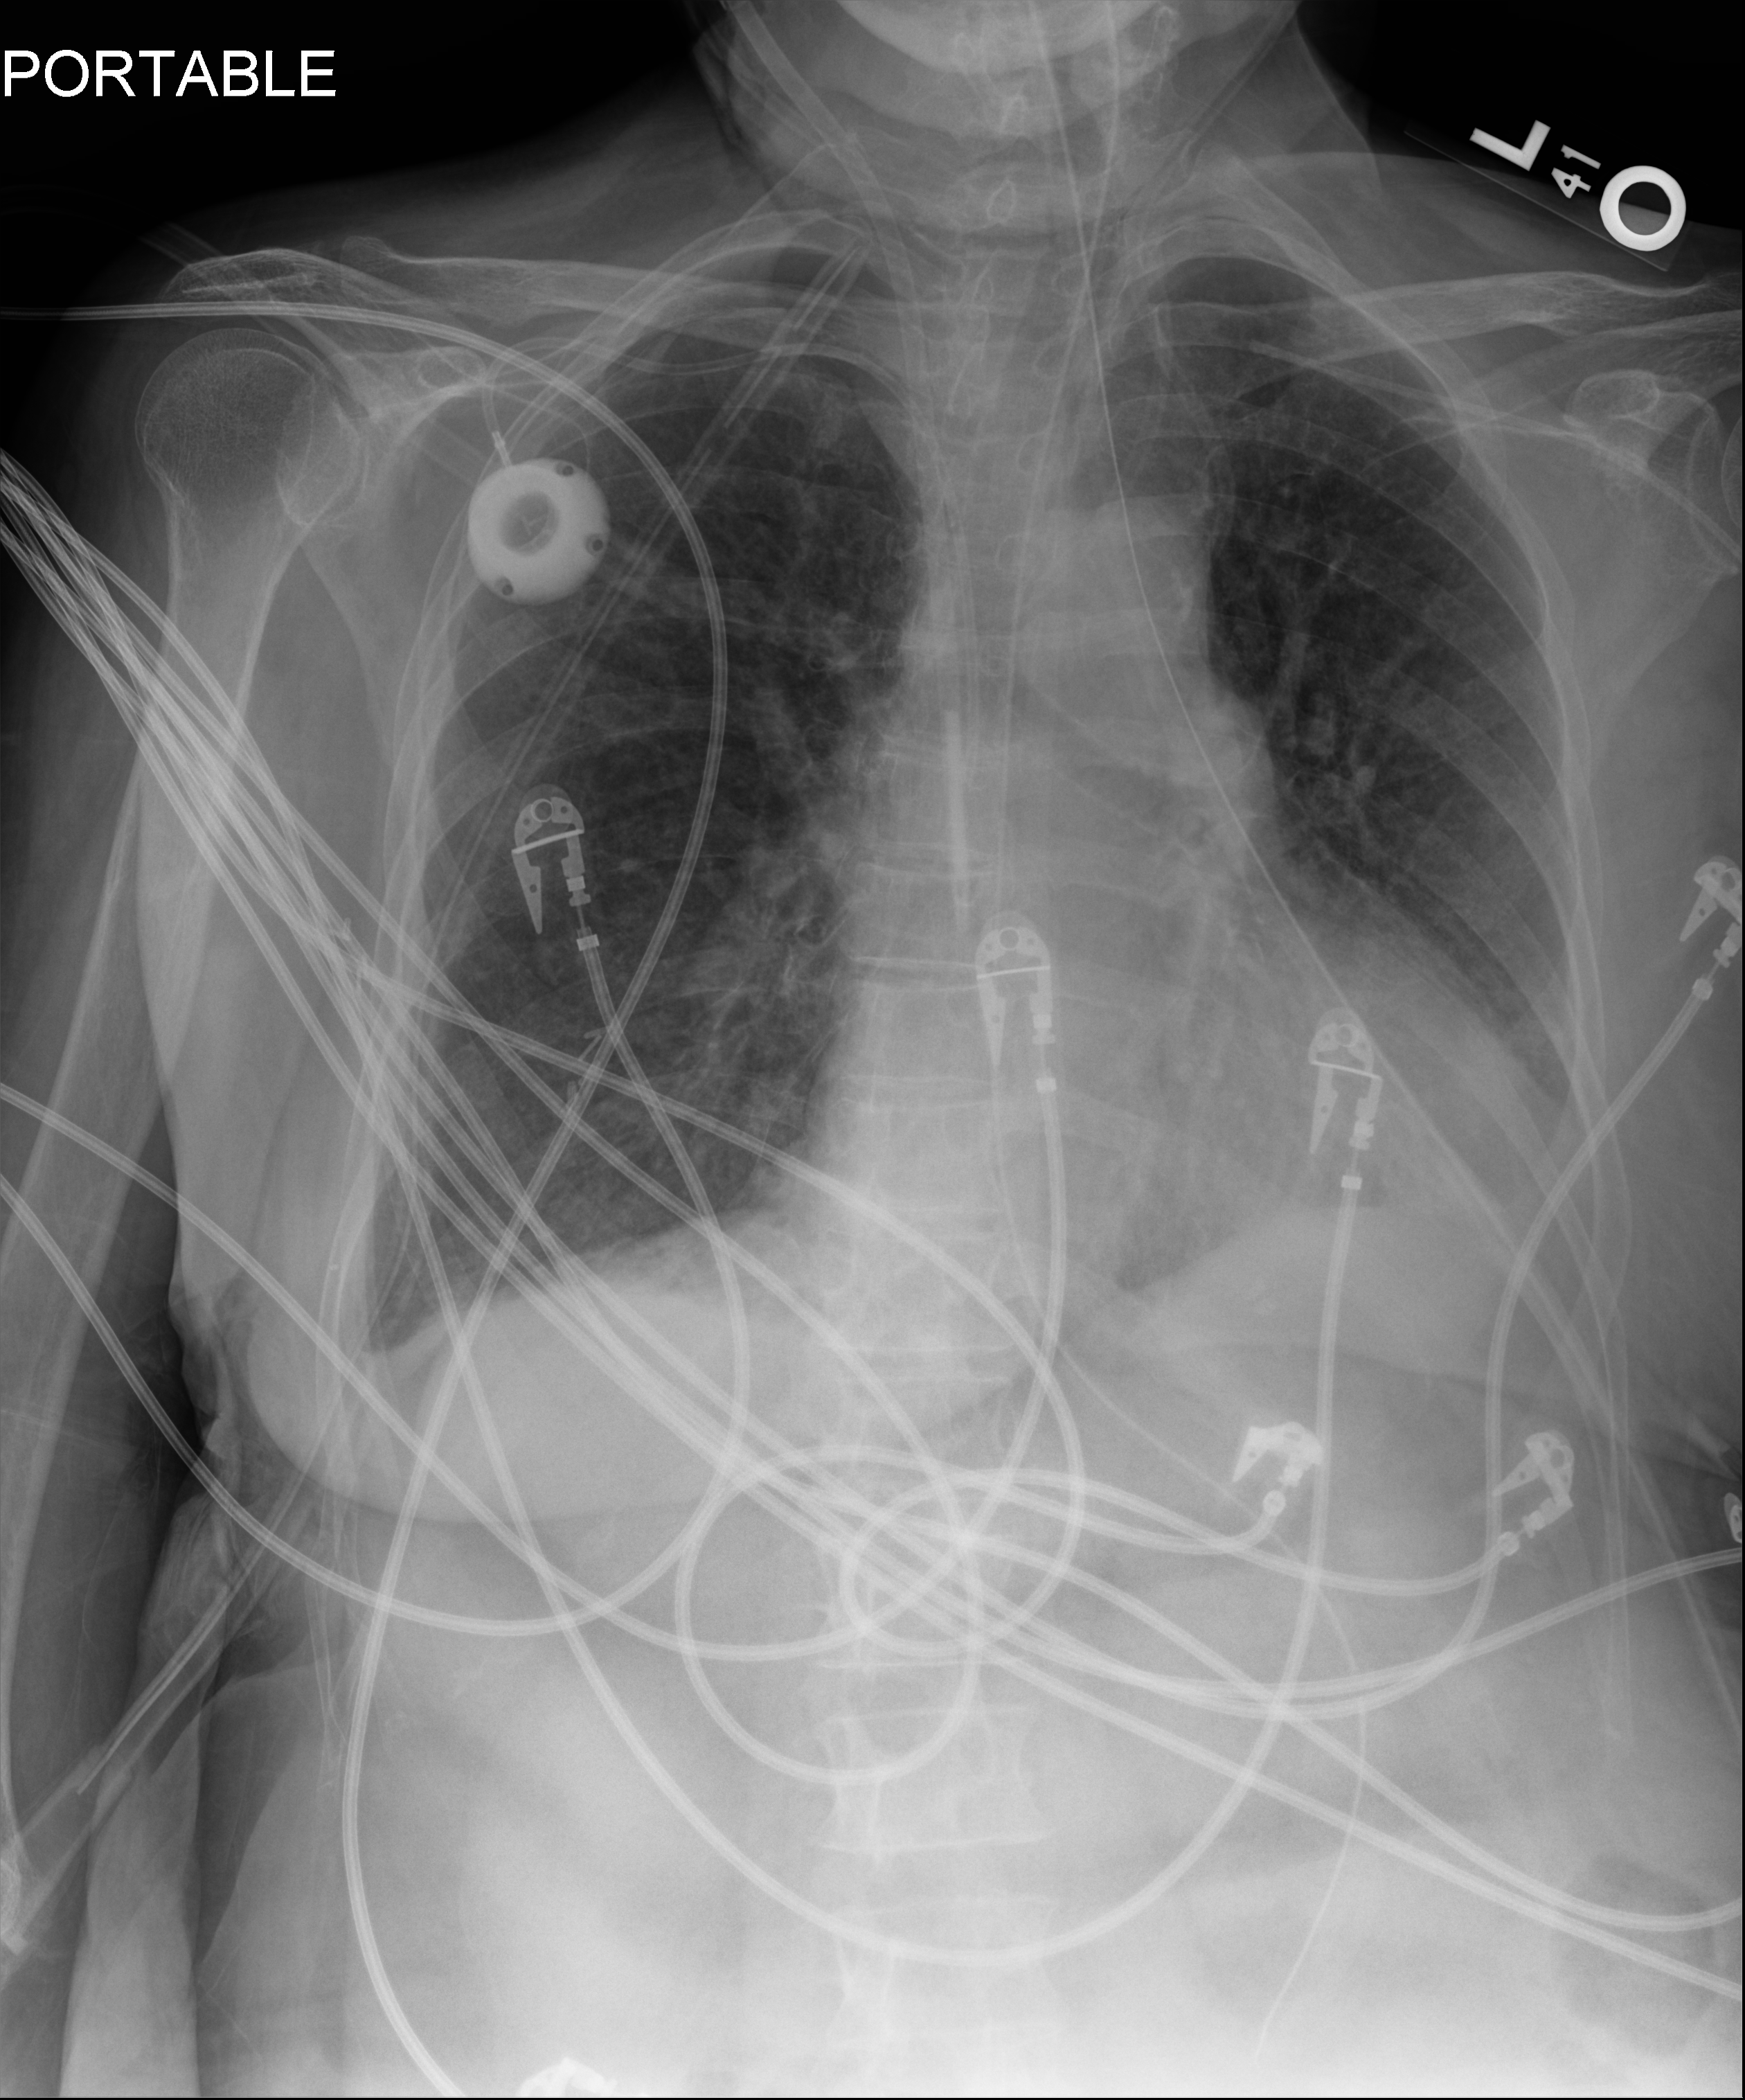
Chest radiograph (digital radiography), anteroposterior (AP) projection. Female patient hospitalised with COVID-19, age 60–74 years.
Hospital-stay facts (about this admission, not read from this image; timing relative to this image not recorded): mechanically ventilated during this hospital stay: yes; hypertension (admission record): yes; admitted to intensive care during this hospital stay: yes.